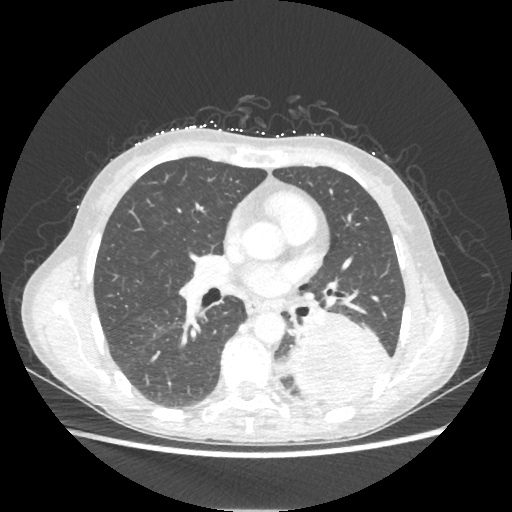
Chest CT, one axial slice; position 117 of 221 along the scan axis; reconstruction kernel STANDARD; 80 kVp; lung window (W 1500 / L -600 HU); 1.25 mm slice thickness; 512 × 512 image matrix. Female patient, age 53 years. Case-level facts recorded for this patient, not image findings: clinical TNM (as recorded): T3 N0 M0.
Annotated regions visible in this slice (rectangle marked by the reading radiologist):
- lung tumour (recorded histology: adenocarcinoma): bounding box <284,304,392,403> (left, top, right, bottom; pixels)